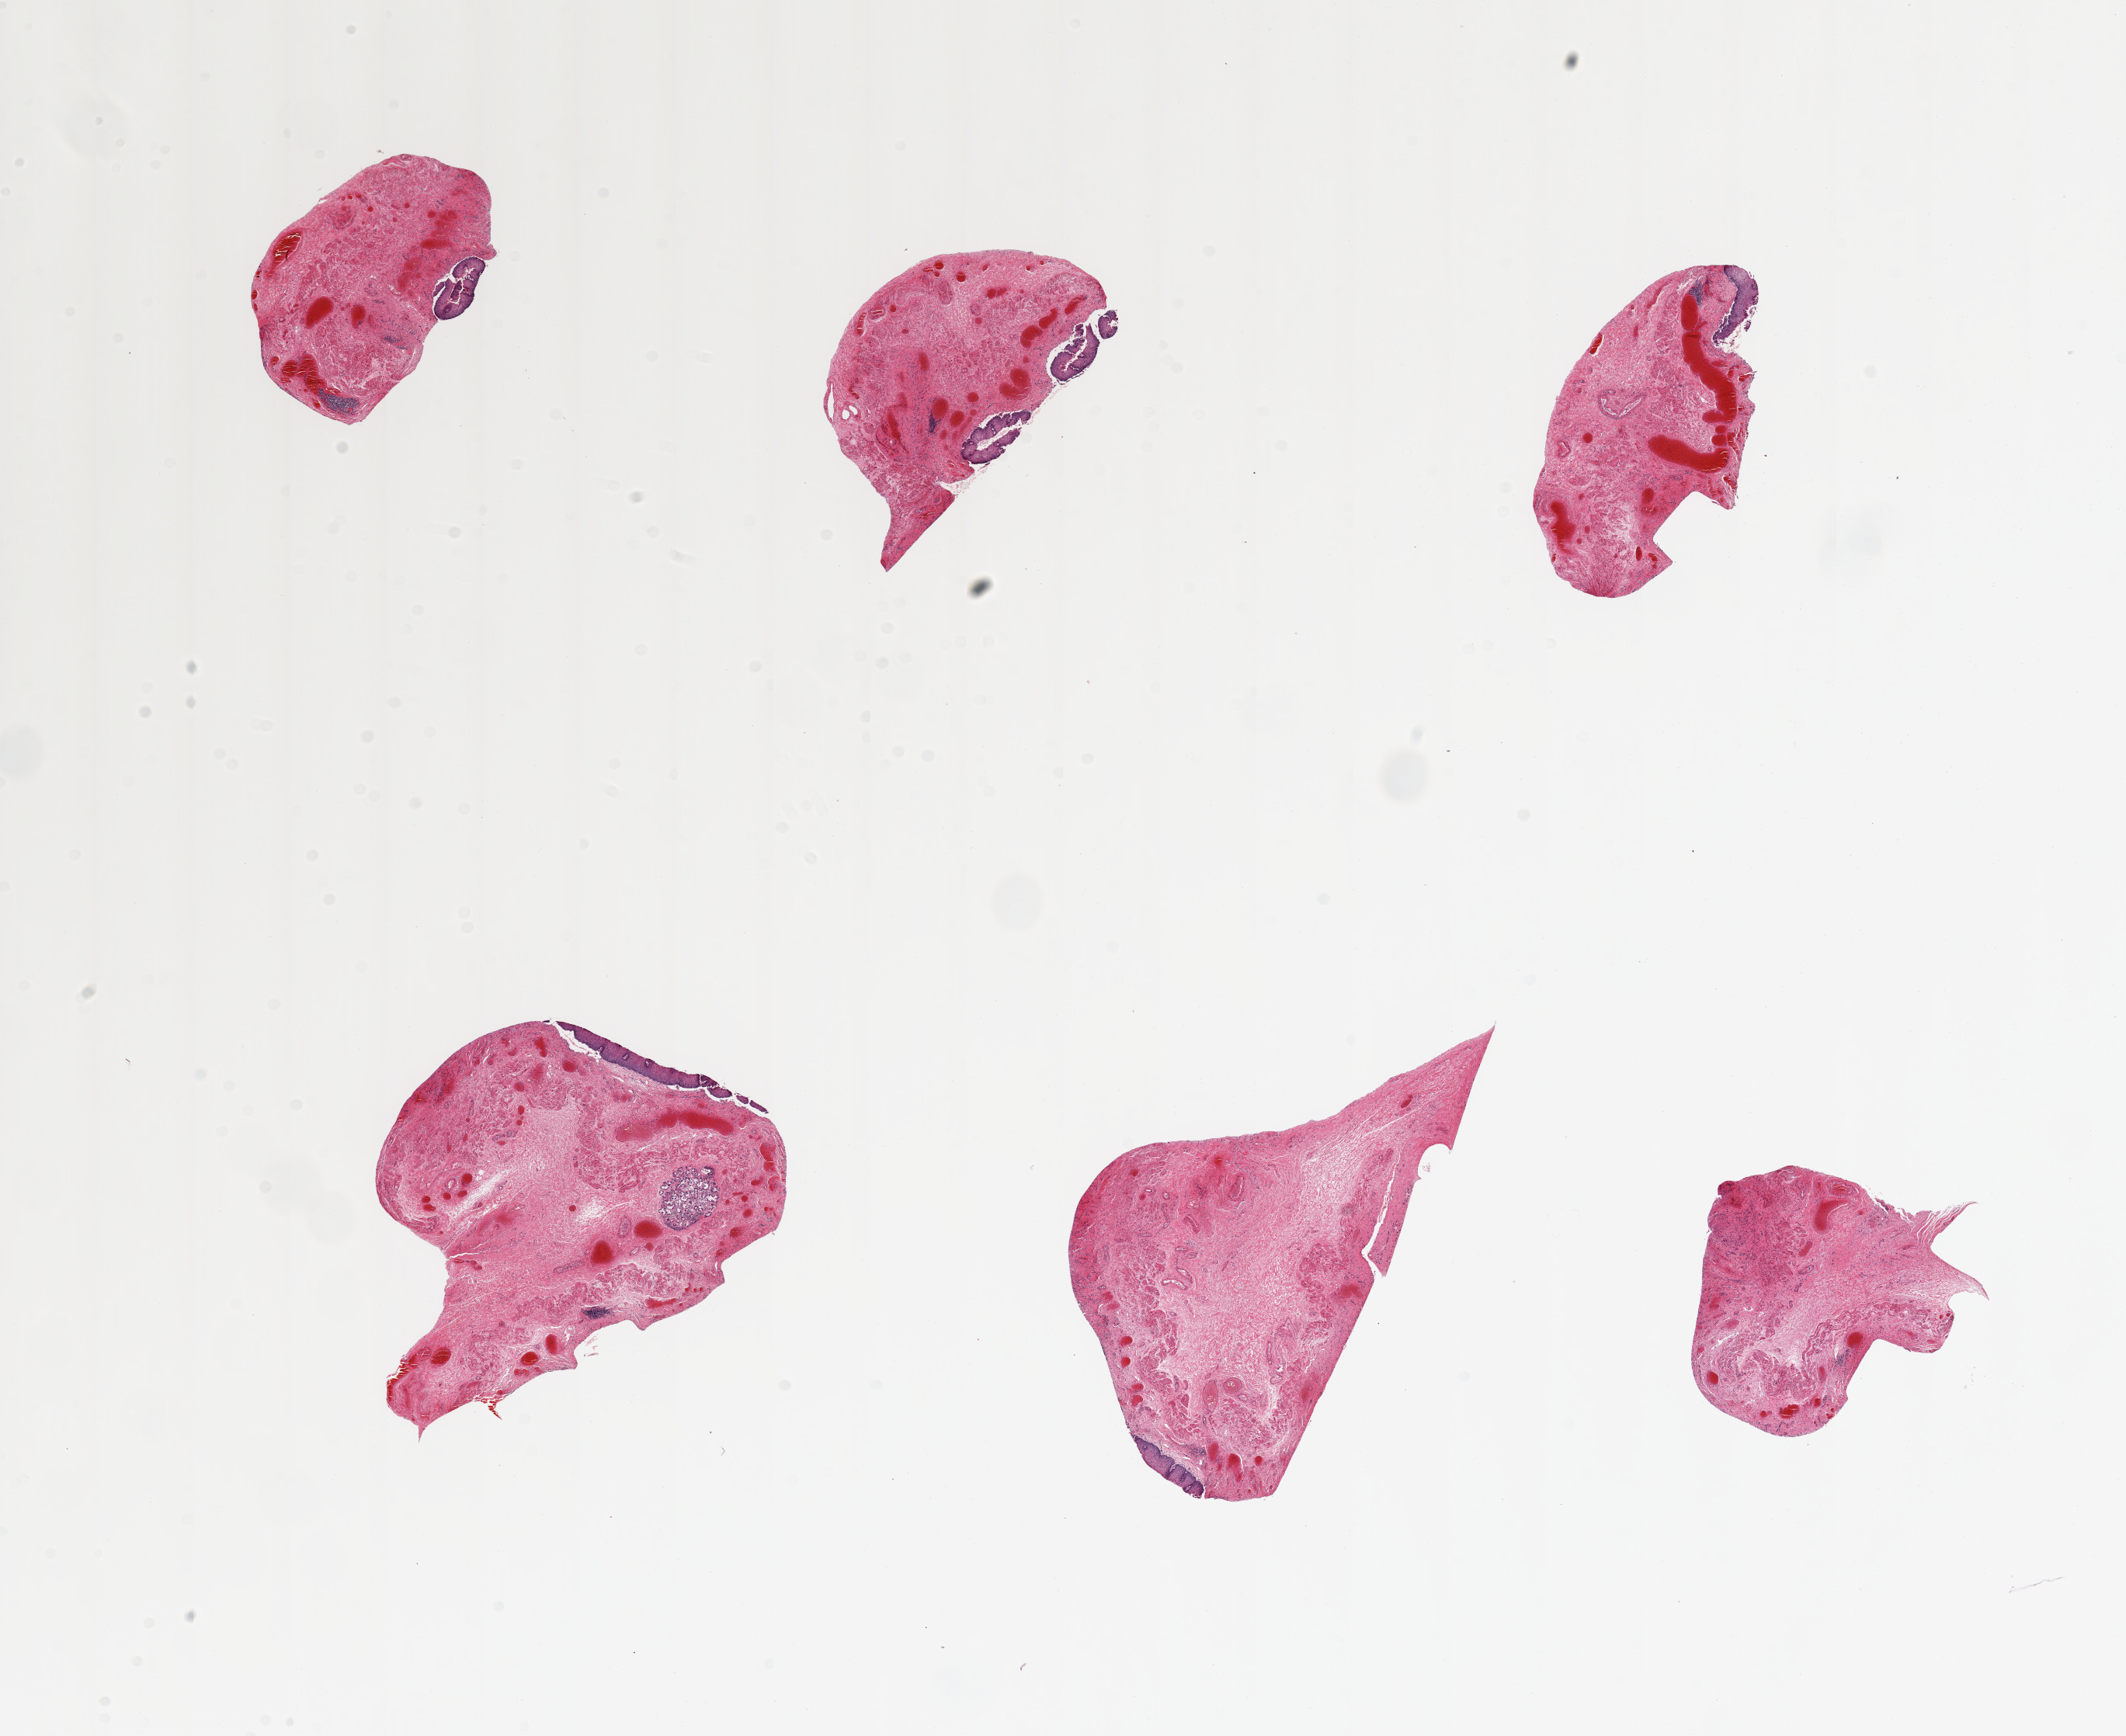
Haematoxylin and eosin whole-slide image — low-resolution overview of the scanned area, about 21.7 x 17.7 mm.
Specimen: PAXgene-fixed paraffin-embedded (PFPE) section; target tissue: esophageal mucous membrane; tissue donor sample.